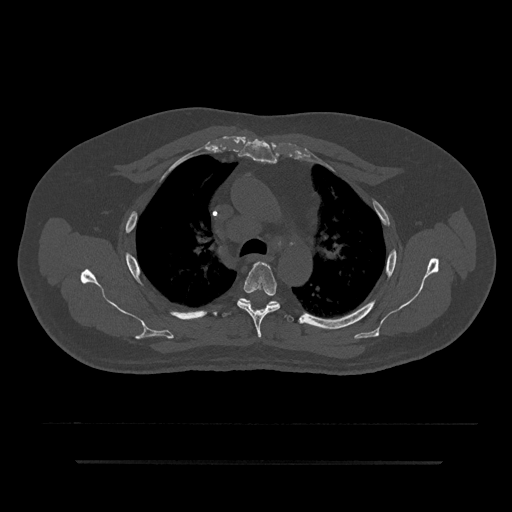
CT including the spine, one axial slice; position 609 of 797 along the scan axis; 120 kVp; bone window (W 1800 / L 400 HU); 512 × 512 image matrix. Male patient, age 59 years. From the clinical record (not read from this slice): primary cancer: bile ducts.
Annotated regions visible in this slice (semi-automatic segmentation, software-assisted and operator-edited):
- T4 vertebra: bounding box (x1, y1, x2, y2) in pixels: (237, 262, 280, 338)
- T5 vertebra: (228, 298, 294, 320)